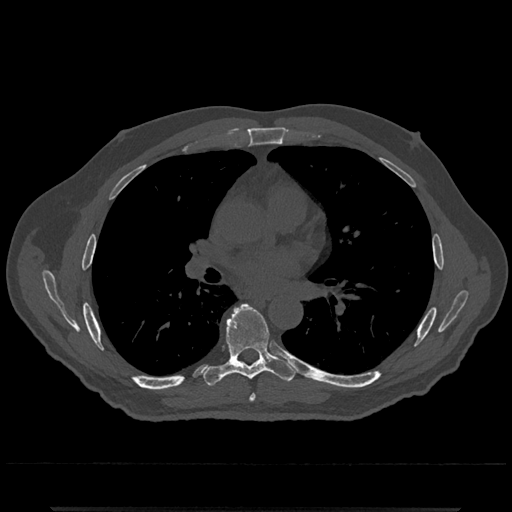
CT including the spine, one axial slice; position 728 of 797 along the scan axis; reconstruction kernel Br40s/3; 120 kVp; bone window (W 1800 / L 400 HU); 512 × 512 image matrix. Male patient, age 67 years. Case-level facts recorded for this patient, not image findings: primary cancer: prostate.
Structures marked on this image (semi-automatic segmentation, software-assisted and operator-edited):
- T6 vertebra: bounding box [x1, y1, x2, y2] px = [249, 394, 256, 402]
- T7 vertebra: [204, 304, 297, 386]